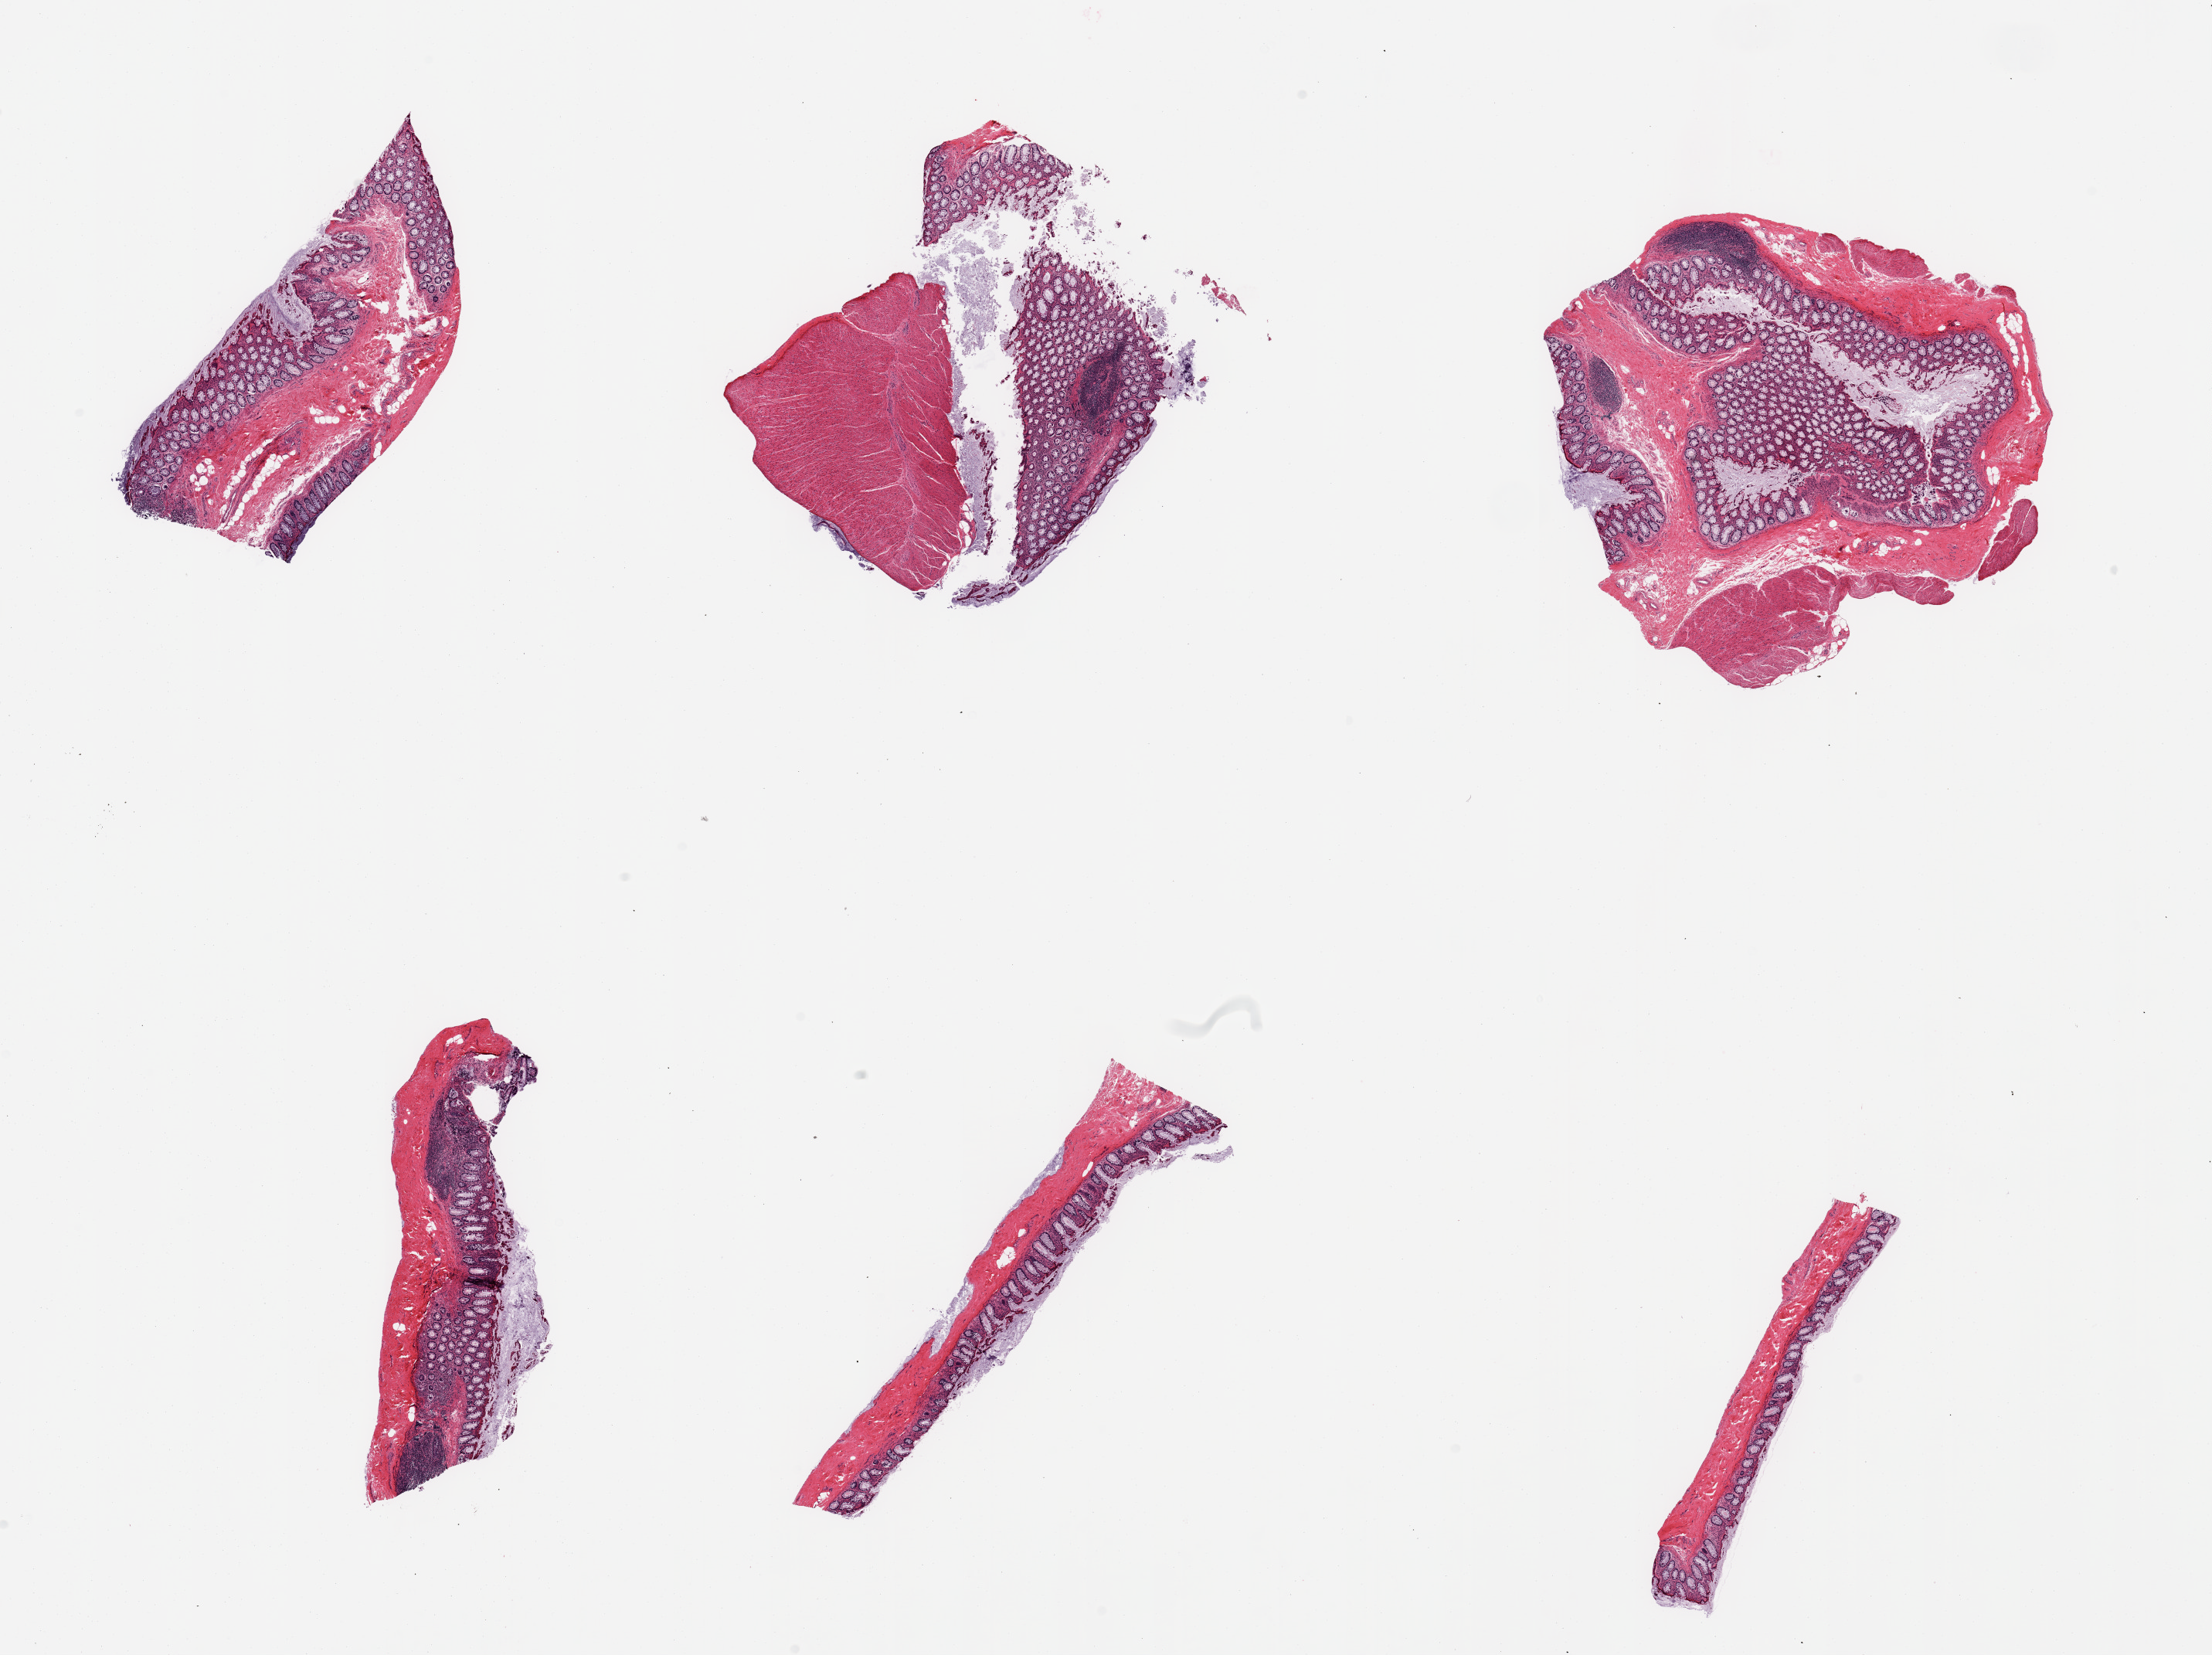
Digitized H&E-stained section, a low-resolution overview of the entire scanned area, about 22.6 x 16.9 mm. PAXgene-fixed paraffin-embedded (PFPE) section. Target tissue: sigmoid colon. Tissue donor sample. Donor sex: male.
Review note (as recorded): 6 pieces: all have mucosa, only 2 have muscle.